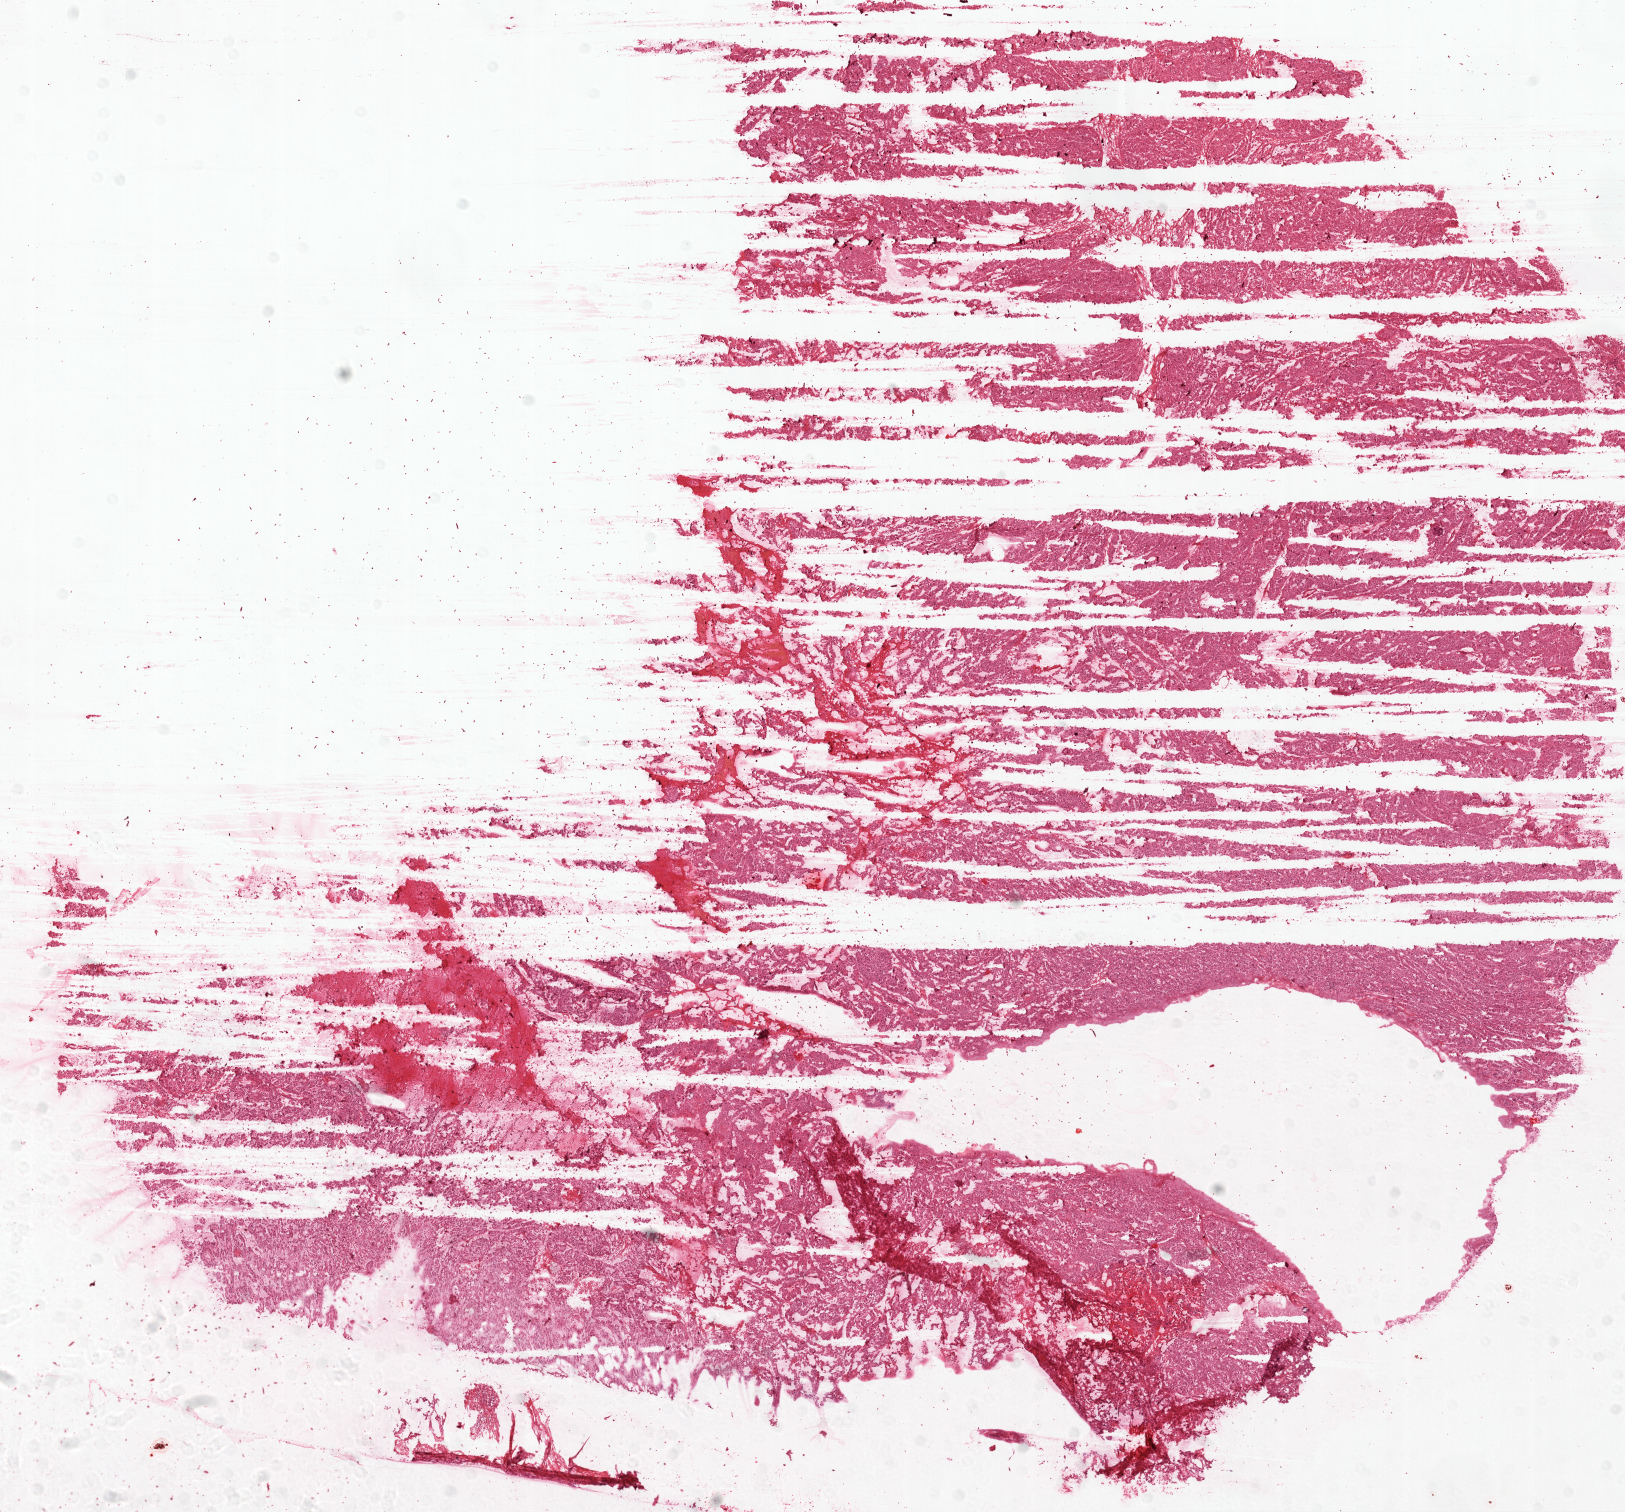
Whole-slide histology image, H&E — a low-resolution overview of the entire scanned area, about 13.0 x 12.1 mm. Frozen section from the top of the tissue portion. Primary tumour sample from the ovary. Patient: female, age at initial diagnosis 60 years. Histologic grade: G3 (poorly differentiated). Slide review estimates, as recorded: tumour cells 98%, tumour nuclei 95%, normal cells 0%, stromal cells 0%, necrosis 2%.
FIGO stage: IIIC. Histologic diagnosis: Serous cystadenocarcinoma, NOS.